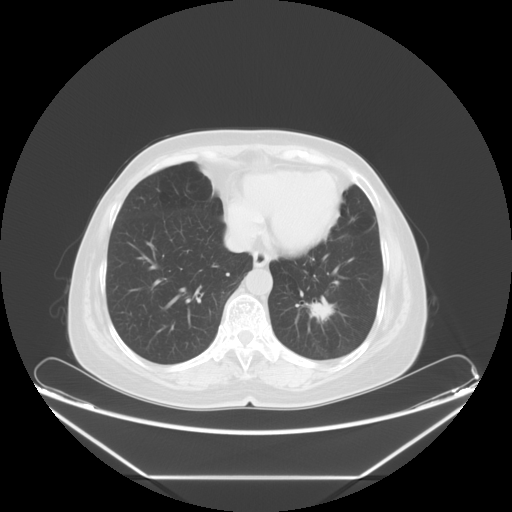
Chest CT, one axial slice. Slice 20 of 61 in the series (ordered by position). Lung window (W 1500 / L -600 HU). 512 × 512 image matrix, field of view 451 × 451 mm. Female patient, age 63 years. Case-level facts recorded for this patient, not image findings: clinical TNM (as recorded): T1c N0 M0; histopathological grade: G2-3.
Structures marked on this image (bounding box drawn by a radiologist):
- lung tumour (recorded histology: adenocarcinoma): bounding box [x1, y1, x2, y2] px = [307, 293, 339, 327]